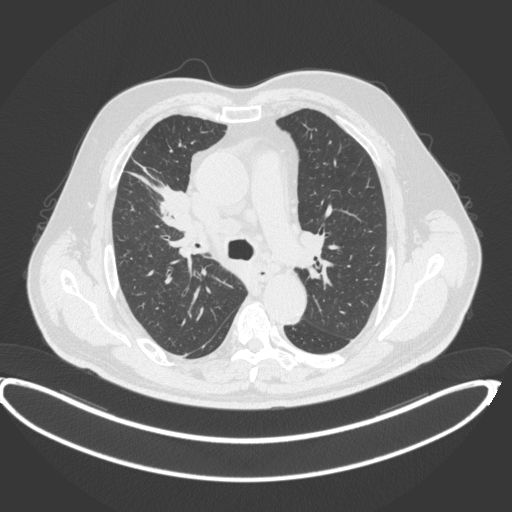
Chest CT, one axial slice; position 272 of 395 along the scan axis; 120 kVp; lung window (W 1500 / L -600 HU); 1 mm slice thickness; 512 × 512 image matrix, field of view 448 × 448 mm. Male patient, age 62 years. From the clinical record (not read from this slice): clinical TNM (as recorded): T1c N3 M1c.
Outlined on this slice (rectangle marked by the reading radiologist):
- lung tumour (recorded histology: adenocarcinoma): bounding box (x1, y1, x2, y2) in pixels: (151, 177, 193, 232)